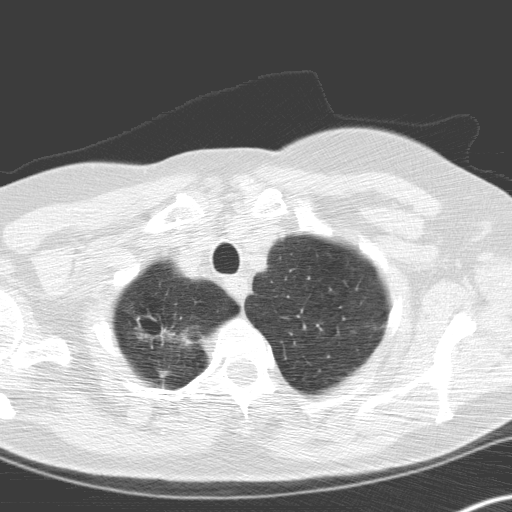
Axial slice from a low-dose chest CT screening exam. Second annual screen. Lung window (W 1500 / L -600 HU). 3.2 mm slice thickness. Slice 26 of 166 in the series. Female, age 60 years at enrolment. Current smoker at enrolment.
Expert reader's lesion annotation, bounding box [x1, y1, x2, y2] px = [128, 306, 208, 377]. Screening reader's record for this exam (one nodule recorded; not confirmed to be the boxed lesion): non-calcified nodule or mass ≥4 mm, right upper lobe, 12 × 8 mm, spiculated (stellate) margins, soft tissue attenuation, pre-existing on the prior screen: no. Official screen result: positive, other.